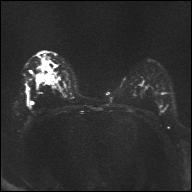
Breast MRI, one axial slice; slice 20 of 32 in the series (ordered by position); diffusion-weighted series; image 2 of 4 stored at this slice position (different b-values; order by instance number); 1.5 T; 4 mm slice thickness; 192 × 192 image matrix, field of view 360 × 360 mm. Female patient.
Structures marked on this image (expert manual segmentation):
- tumour on diffusion-weighted imaging: bounding box (x1, y1, x2, y2) in pixels: (39, 66, 52, 83)